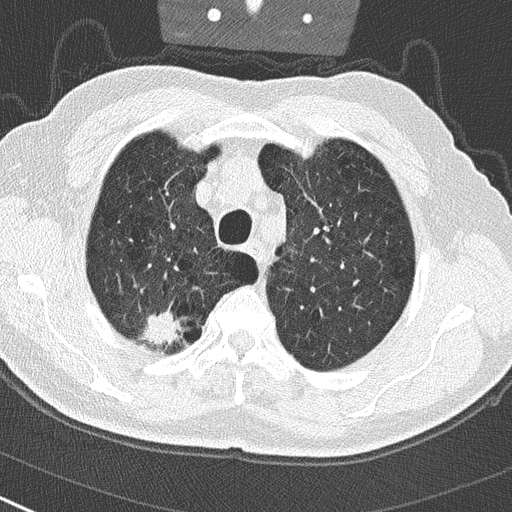
Low-dose screening chest CT, axial slice, baseline screening round, lung window (W 1500 / L -600 HU), 2 mm slice thickness, lung (sharp) reconstruction kernel (B50f), 120 kVp, slice 56 of 290 in the series. Male participant, aged 65 years at enrolment. Current smoker at enrolment.
Expert reader's lesion annotation, bounding box (x1, y1, x2, y2) in pixels: (134, 303, 187, 353). Screening reader's record for this exam (one nodule recorded; not confirmed to be the boxed lesion): non-calcified nodule or mass ≥4 mm, right upper lobe, 24 × 19 mm, spiculated (stellate) margins, soft tissue attenuation. Official screen result: positive, change unspecified: nodule(s) >= 4 mm or enlarging nodule(s), mass(es), or other non-specific abnormalities suspicious for lung cancer.